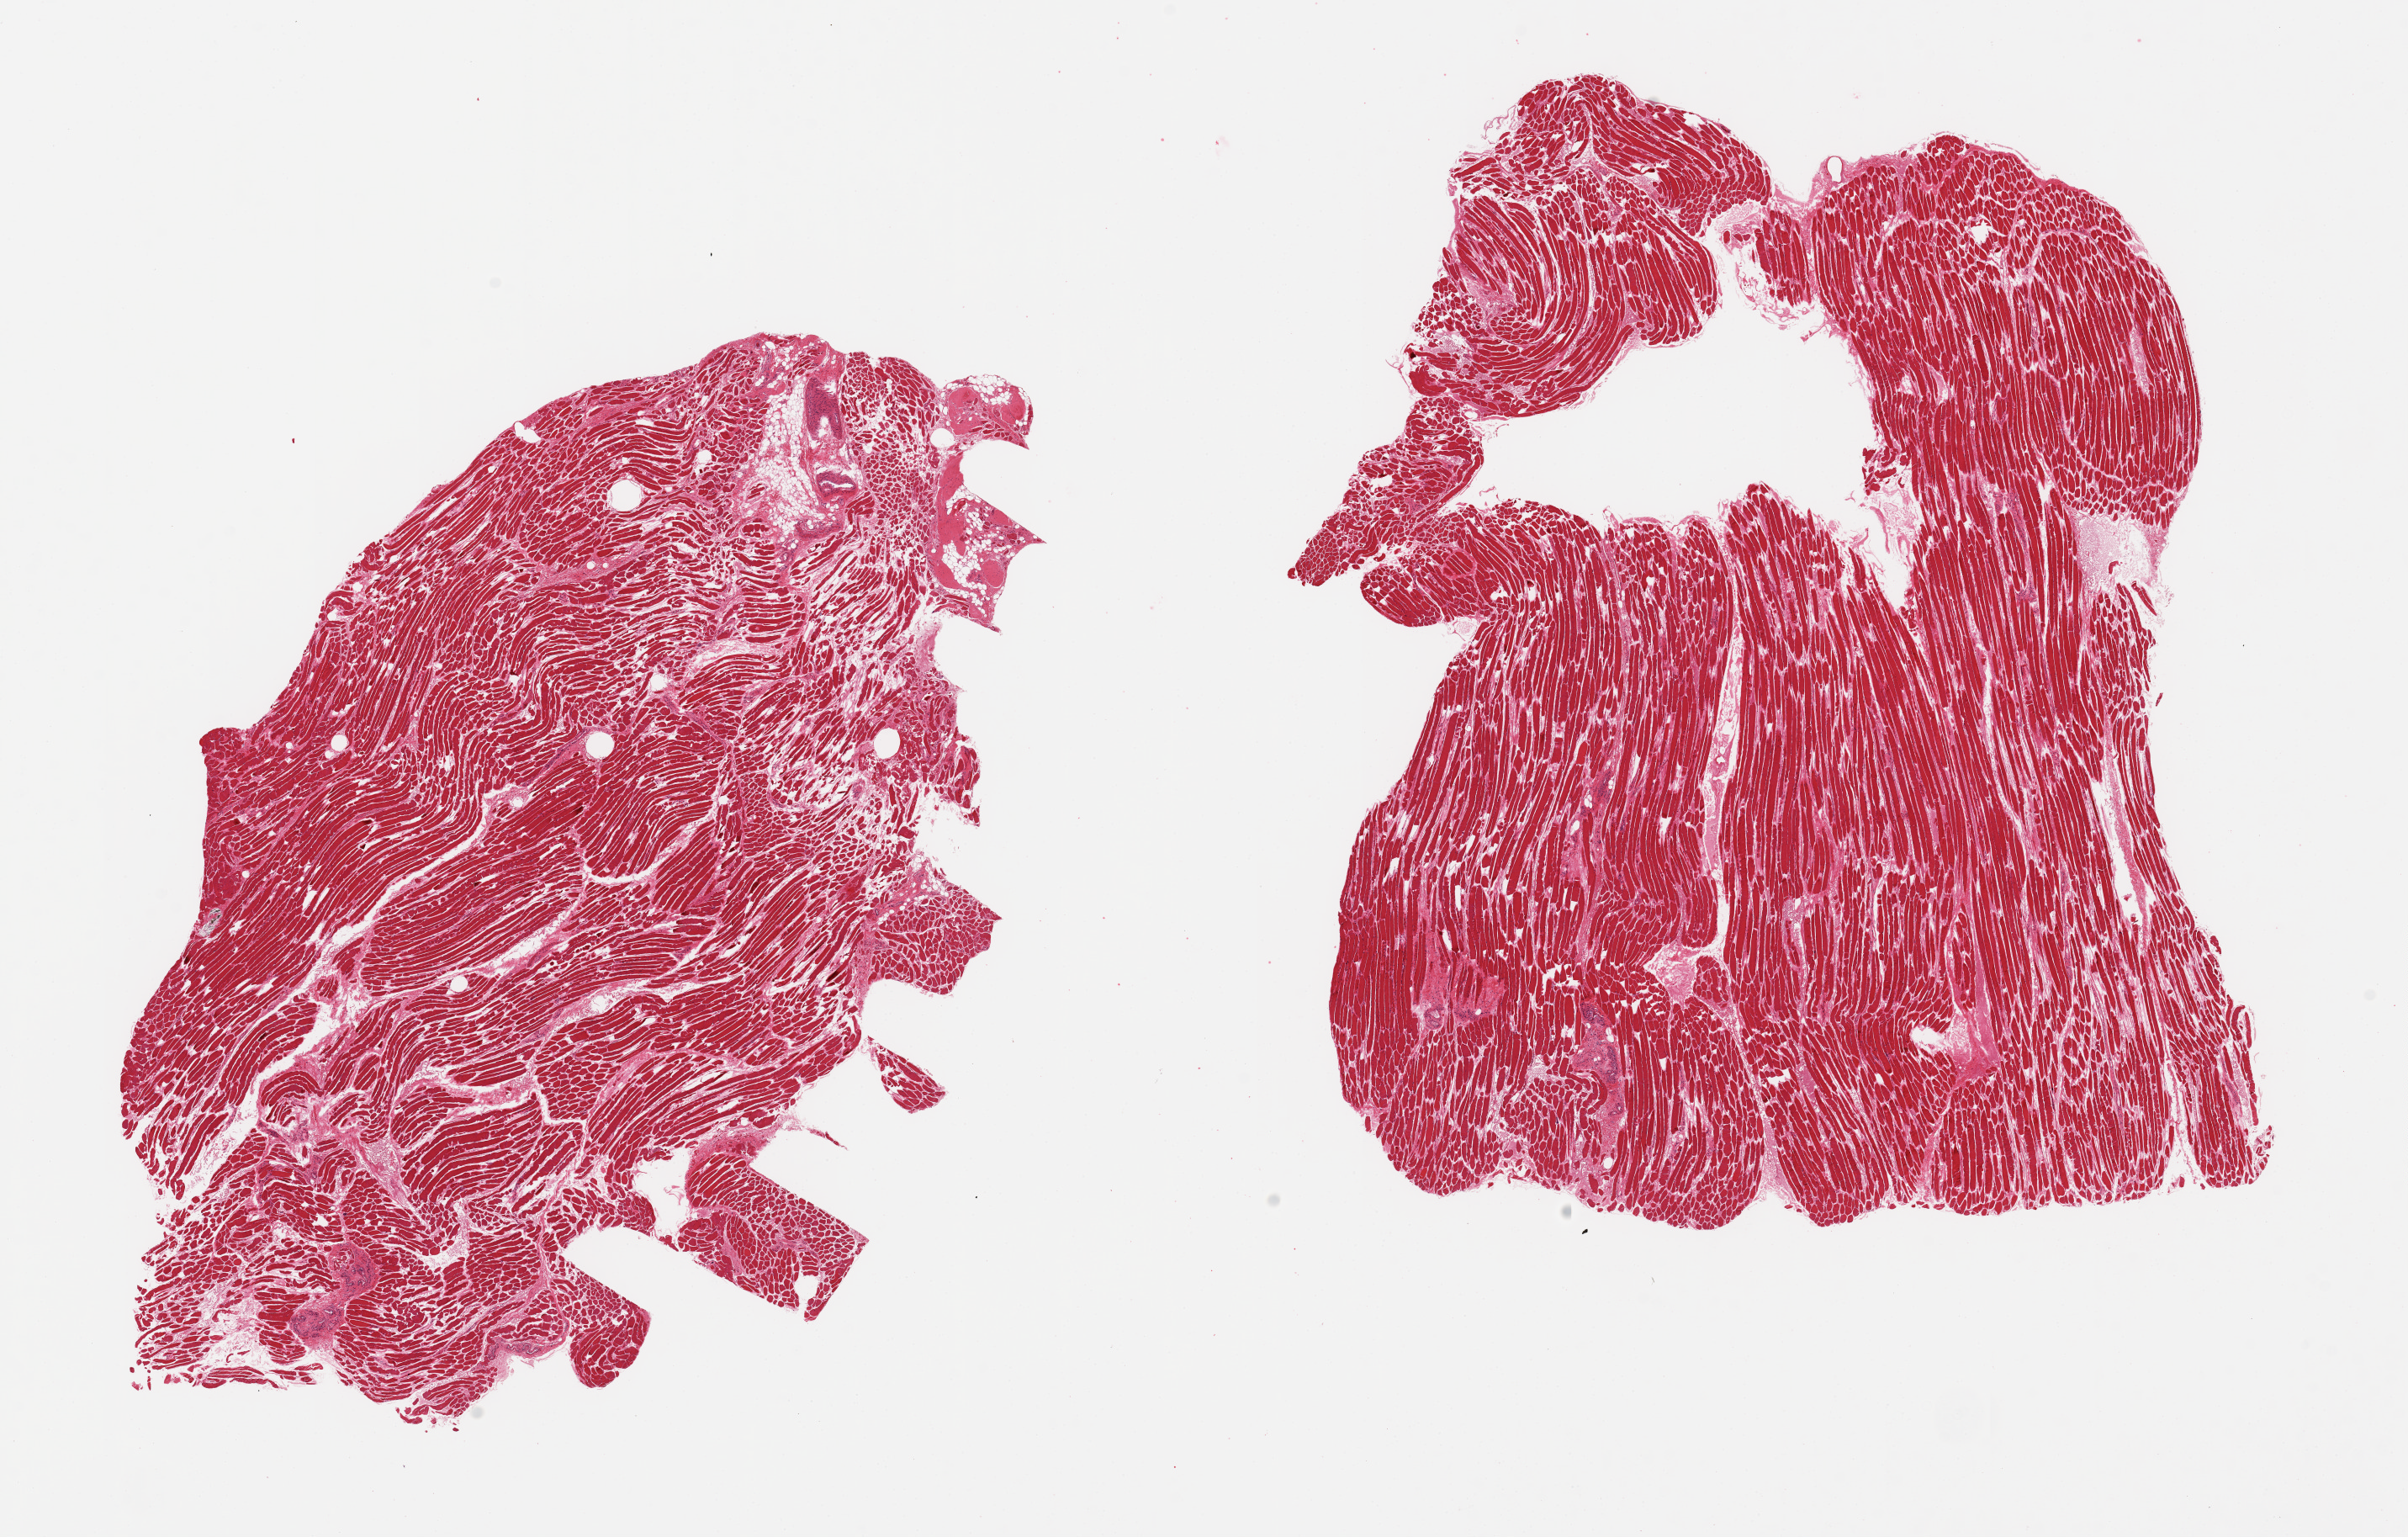
Whole-slide image, hematoxylin and eosin (H&E) stain, brightfield, low-resolution overview of the scanned area, about 22.6 x 14.4 mm (from a 20x scan). PAXgene-fixed paraffin-embedded (PFPE) section. Section of thyroid (target tissue). Donor tissue sample. Donor sex: male.
Pathologist's review note for this sample: 2 pieces; skeletal muscle, not thyroid.